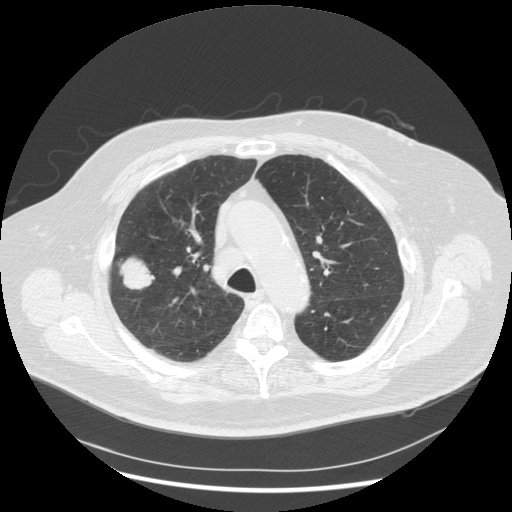
Axial slice from a low-dose chest CT screening exam. Third annual screen. Lung window (W 1500 / L -600 HU). Standard (soft-tissue) reconstruction kernel (STANDARD). Slice 199 of 263 in the series. Male participant, aged 72 years at enrolment. Former smoker at enrolment.
Lesion marked by an expert reader, bounding box (x1, y1, x2, y2) in pixels: (107, 251, 161, 300). Screening reader's record for this exam (one nodule recorded; not confirmed to be the boxed lesion): non-calcified nodule or mass ≥4 mm, right upper lobe, 31 × 31 mm, poorly defined margins, soft tissue attenuation, pre-existing on the prior screen: no. Later outcome: lung cancer diagnosed 70 days after this screen — squamous cell carcinoma, NOS, right upper lobe, poorly differentiated (G3), stage IIIA (AJCC 6th edition), 19 mm at pathology.